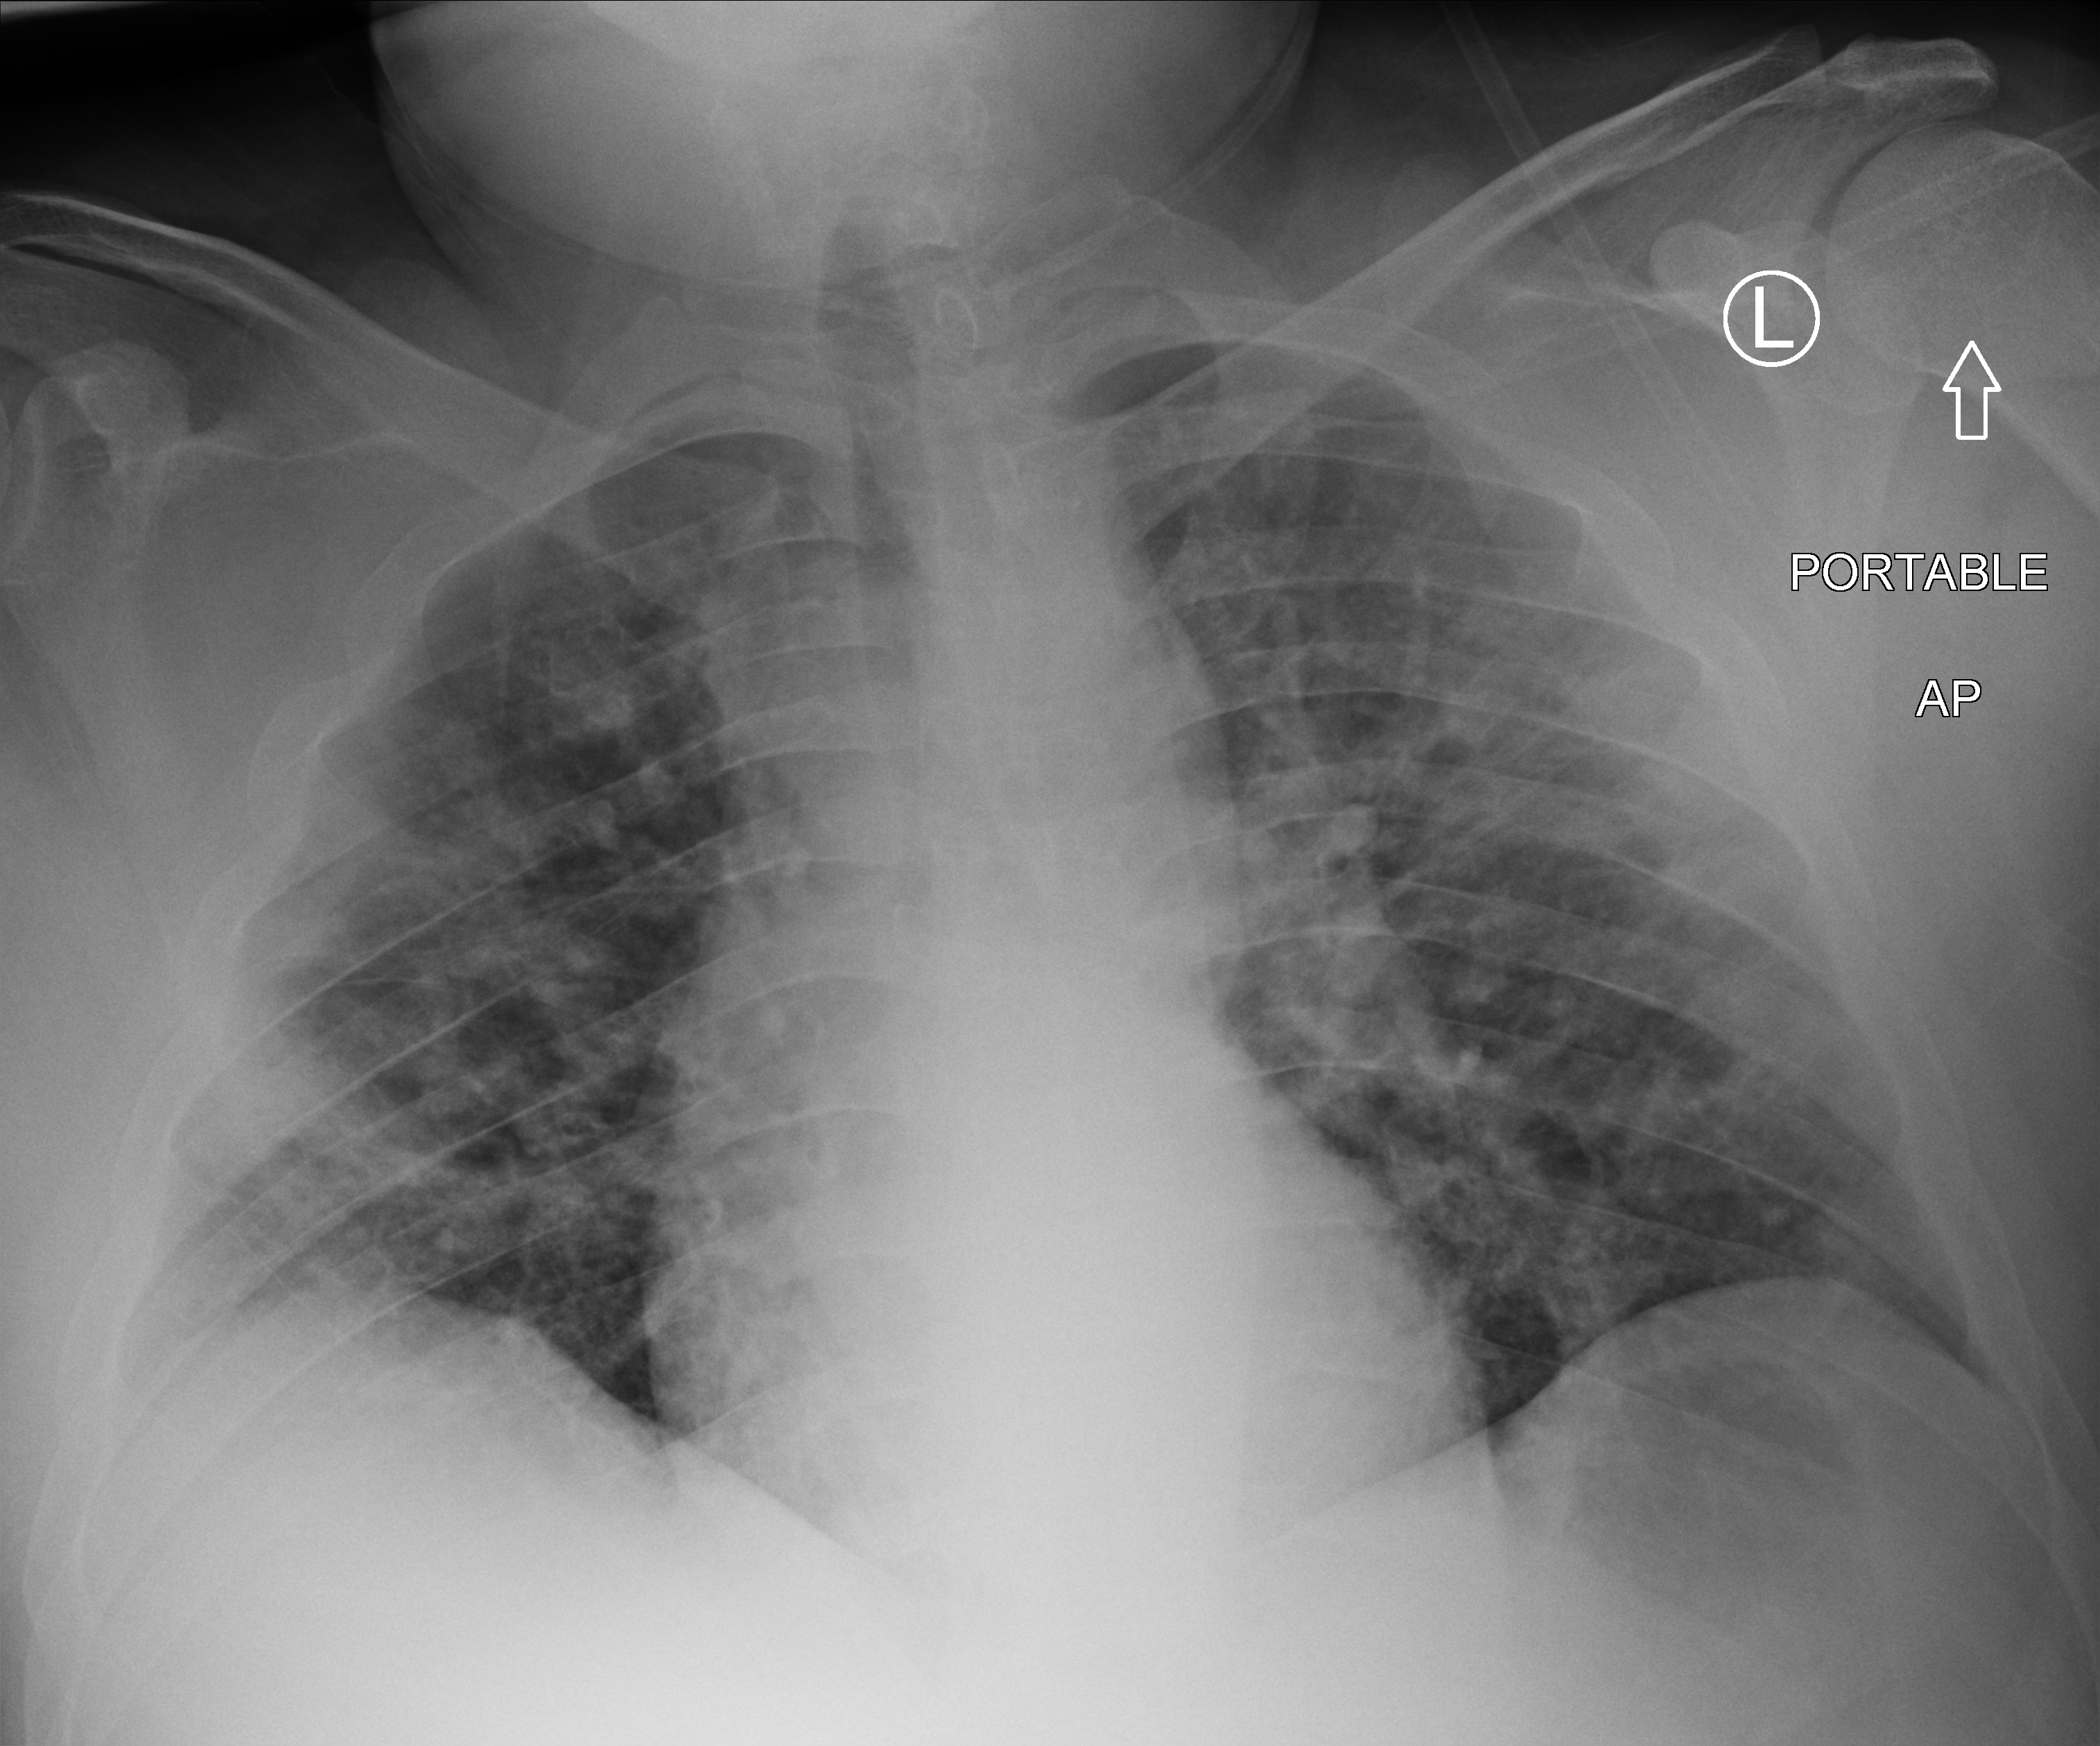
Bedside chest radiograph (computed radiography), anteroposterior (AP) projection. Female patient hospitalised with COVID-19, age 18–59 years.
Admission-level facts for this patient (not findings on this image; timing relative to this image not recorded): admitted to intensive care during this hospital stay: yes.